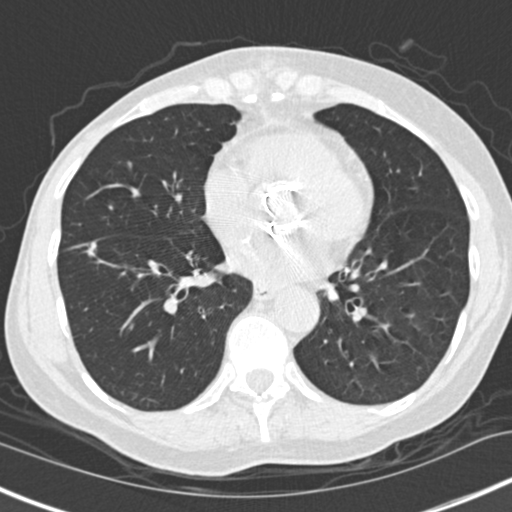
Low-dose screening chest CT, one axial slice; slice 63 of 160 in the series (ordered by position); reconstruction kernel B30f; 120 kVp; lung window (W 1500 / L -600 HU); 2 mm slice thickness; 512 × 512 image matrix, field of view 307 × 307 mm.
Structures marked on this image (manually delineated by an expert):
- lesion 1 (tumor, lower lobe of right lung): box from (x=87, y=242) to (x=96, y=256) px